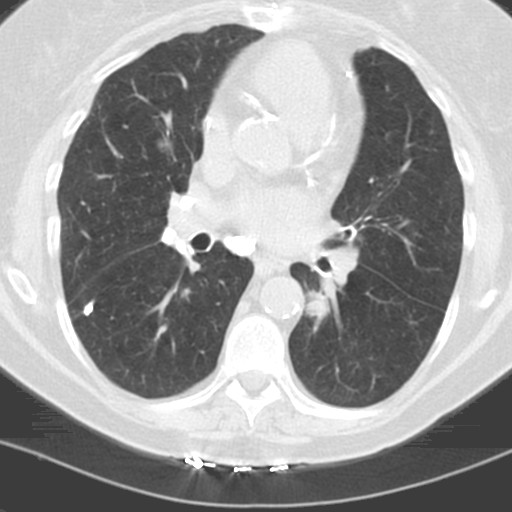
Chest CT (low-dose screening protocol), one axial image, first (baseline) screen, lung window (W 1500 / L -600 HU), standard (soft-tissue) reconstruction kernel (C), 120 kVp, slice 64 of 121 in the series. Female, age 60 years at enrolment. Former smoker at enrolment.
- Expert-annotated lung lesion, bounding box (x1, y1, x2, y2) in pixels: (293, 282, 340, 333).
- The screening reader recorded 3 non-calcified nodules or masses ≥4 mm on this exam; which of them this box marks is not recorded.